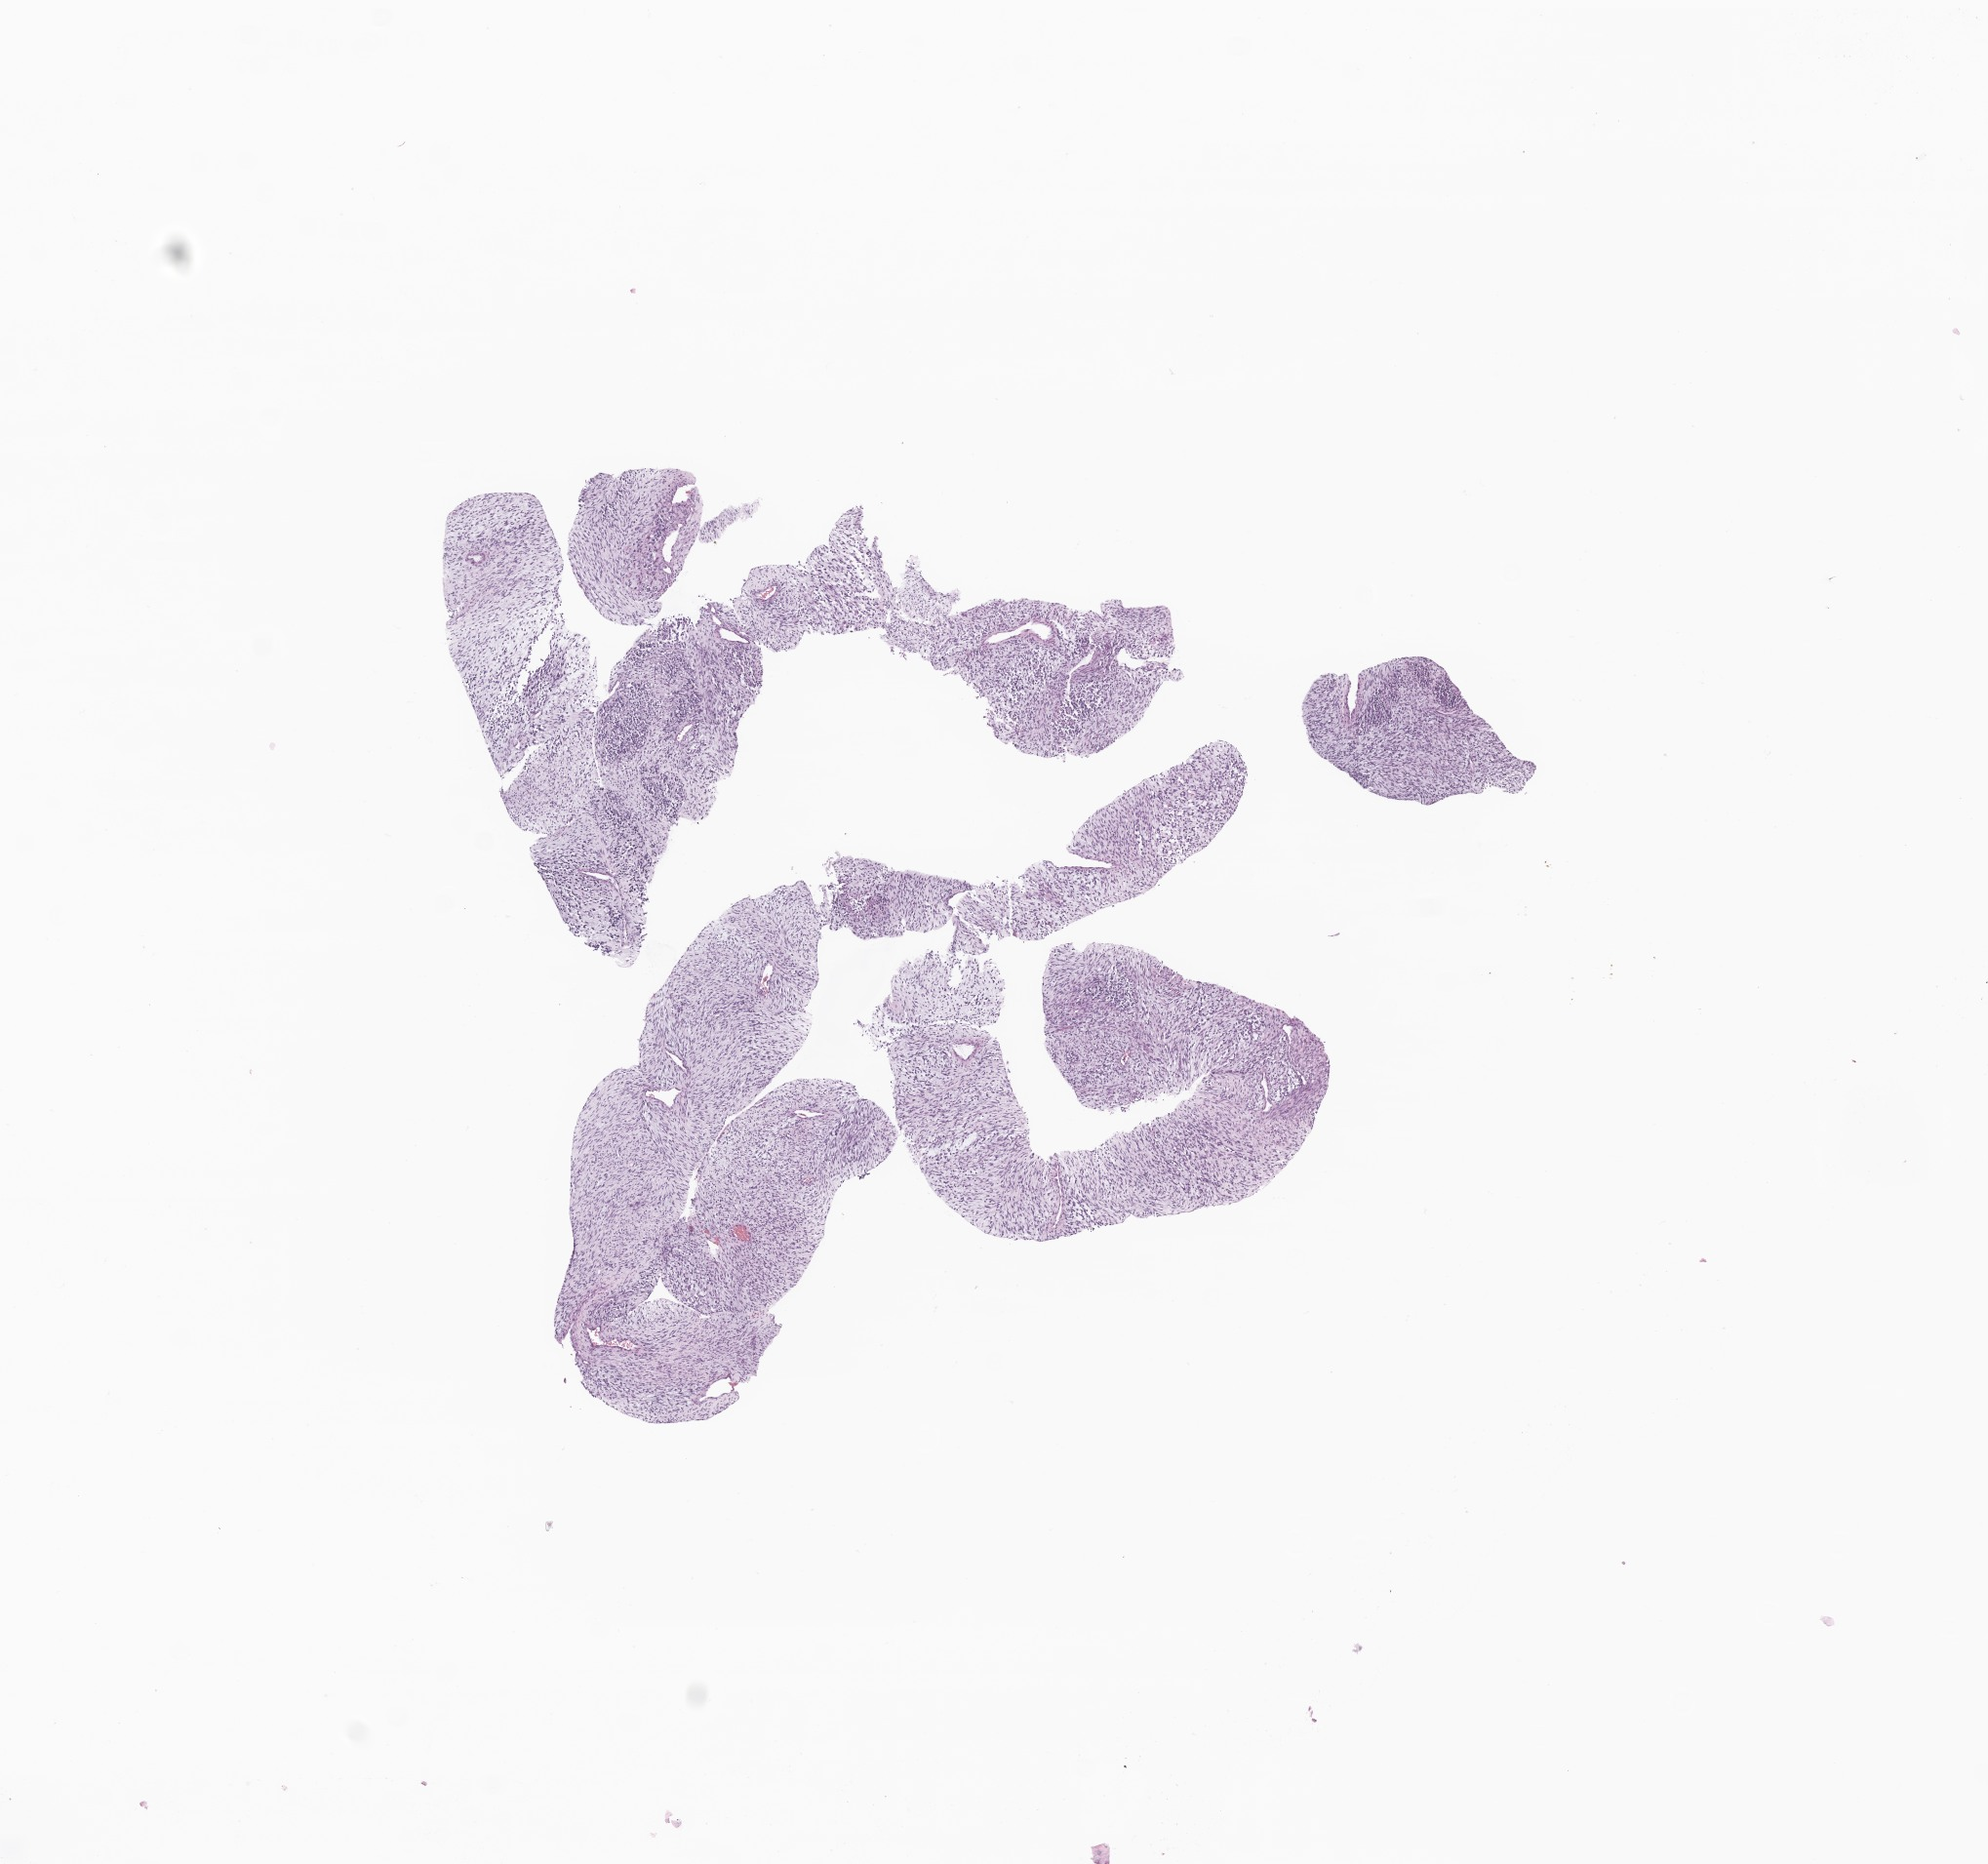
Whole-slide image, haematoxylin and eosin stain of tumor tissue from the soft tissues of head and neck, whole scanned area (about 8.6 x 8.1 mm) shown as a low-resolution overview, formalin-fixed, paraffin-embedded (FFPE) tissue. Male patient, age 39 months (3 years 3 months).
• diagnosis: Rhabdomyosarcoma, NOS